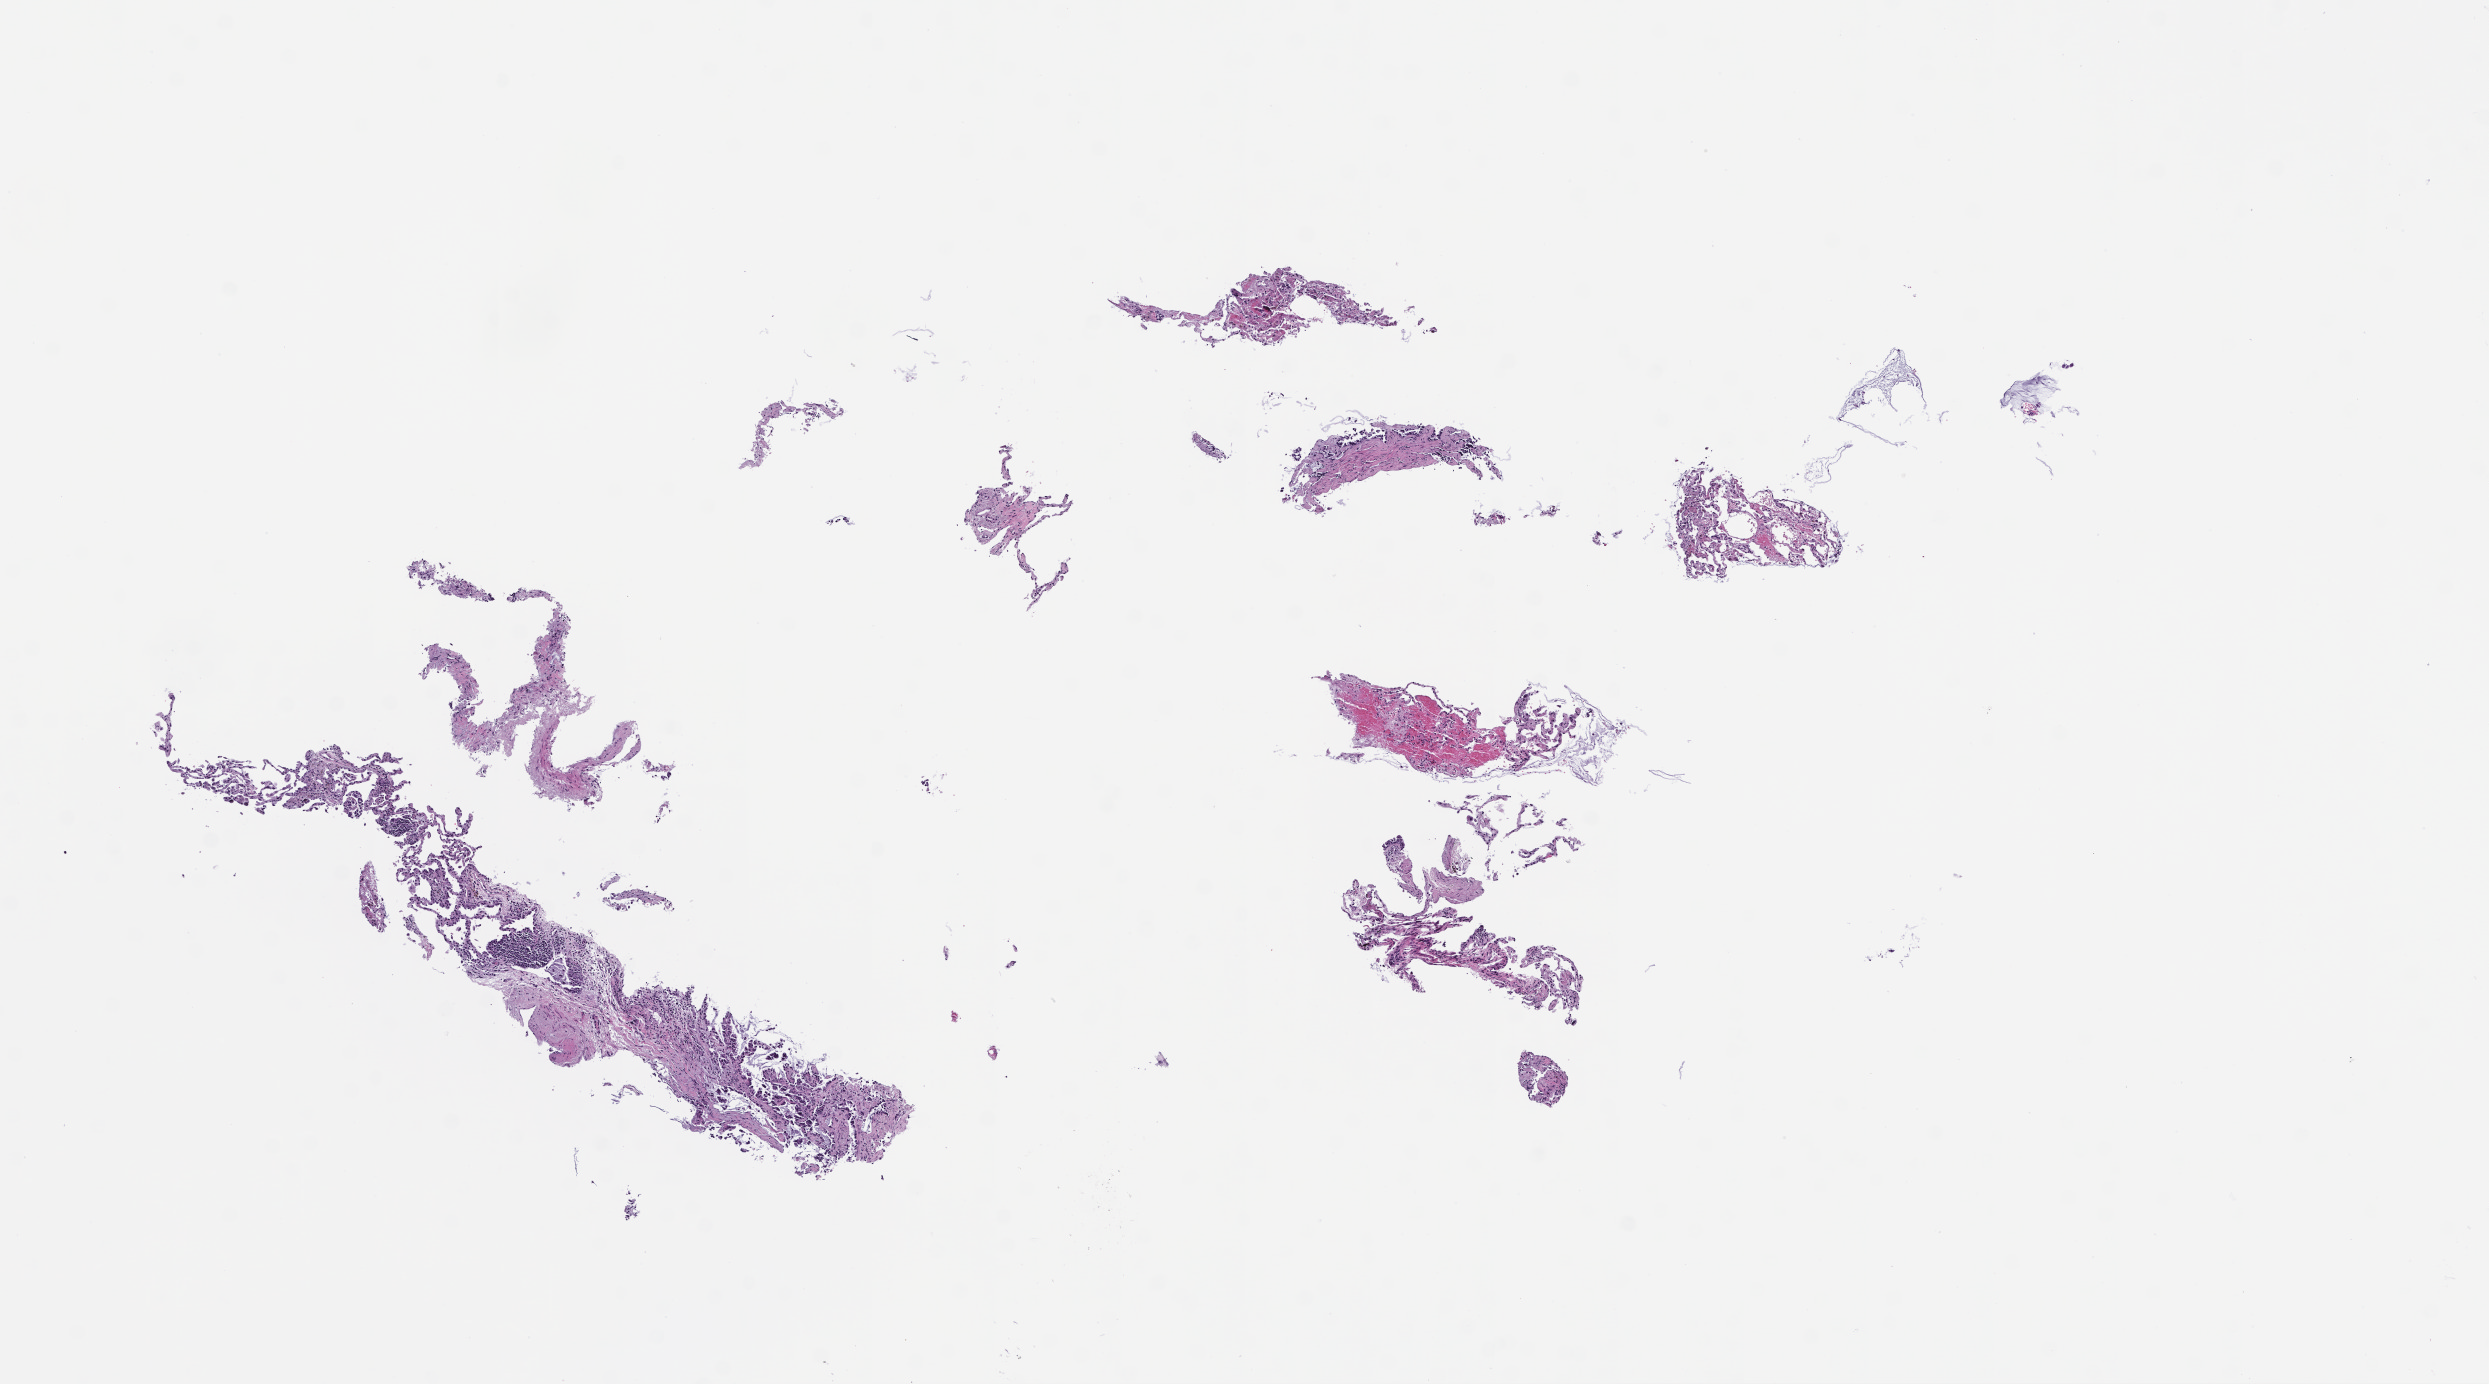
Whole-slide image, H&E stain, whole scanned area (about 10.1 x 5.6 mm) shown as a low-resolution overview, FFPE section, specimen time point: archival tissue. Patient: male.
- this section: metastatic tumor tissue
- primary diagnosis of the patient: Non-Small Cell Lung Carcinoma